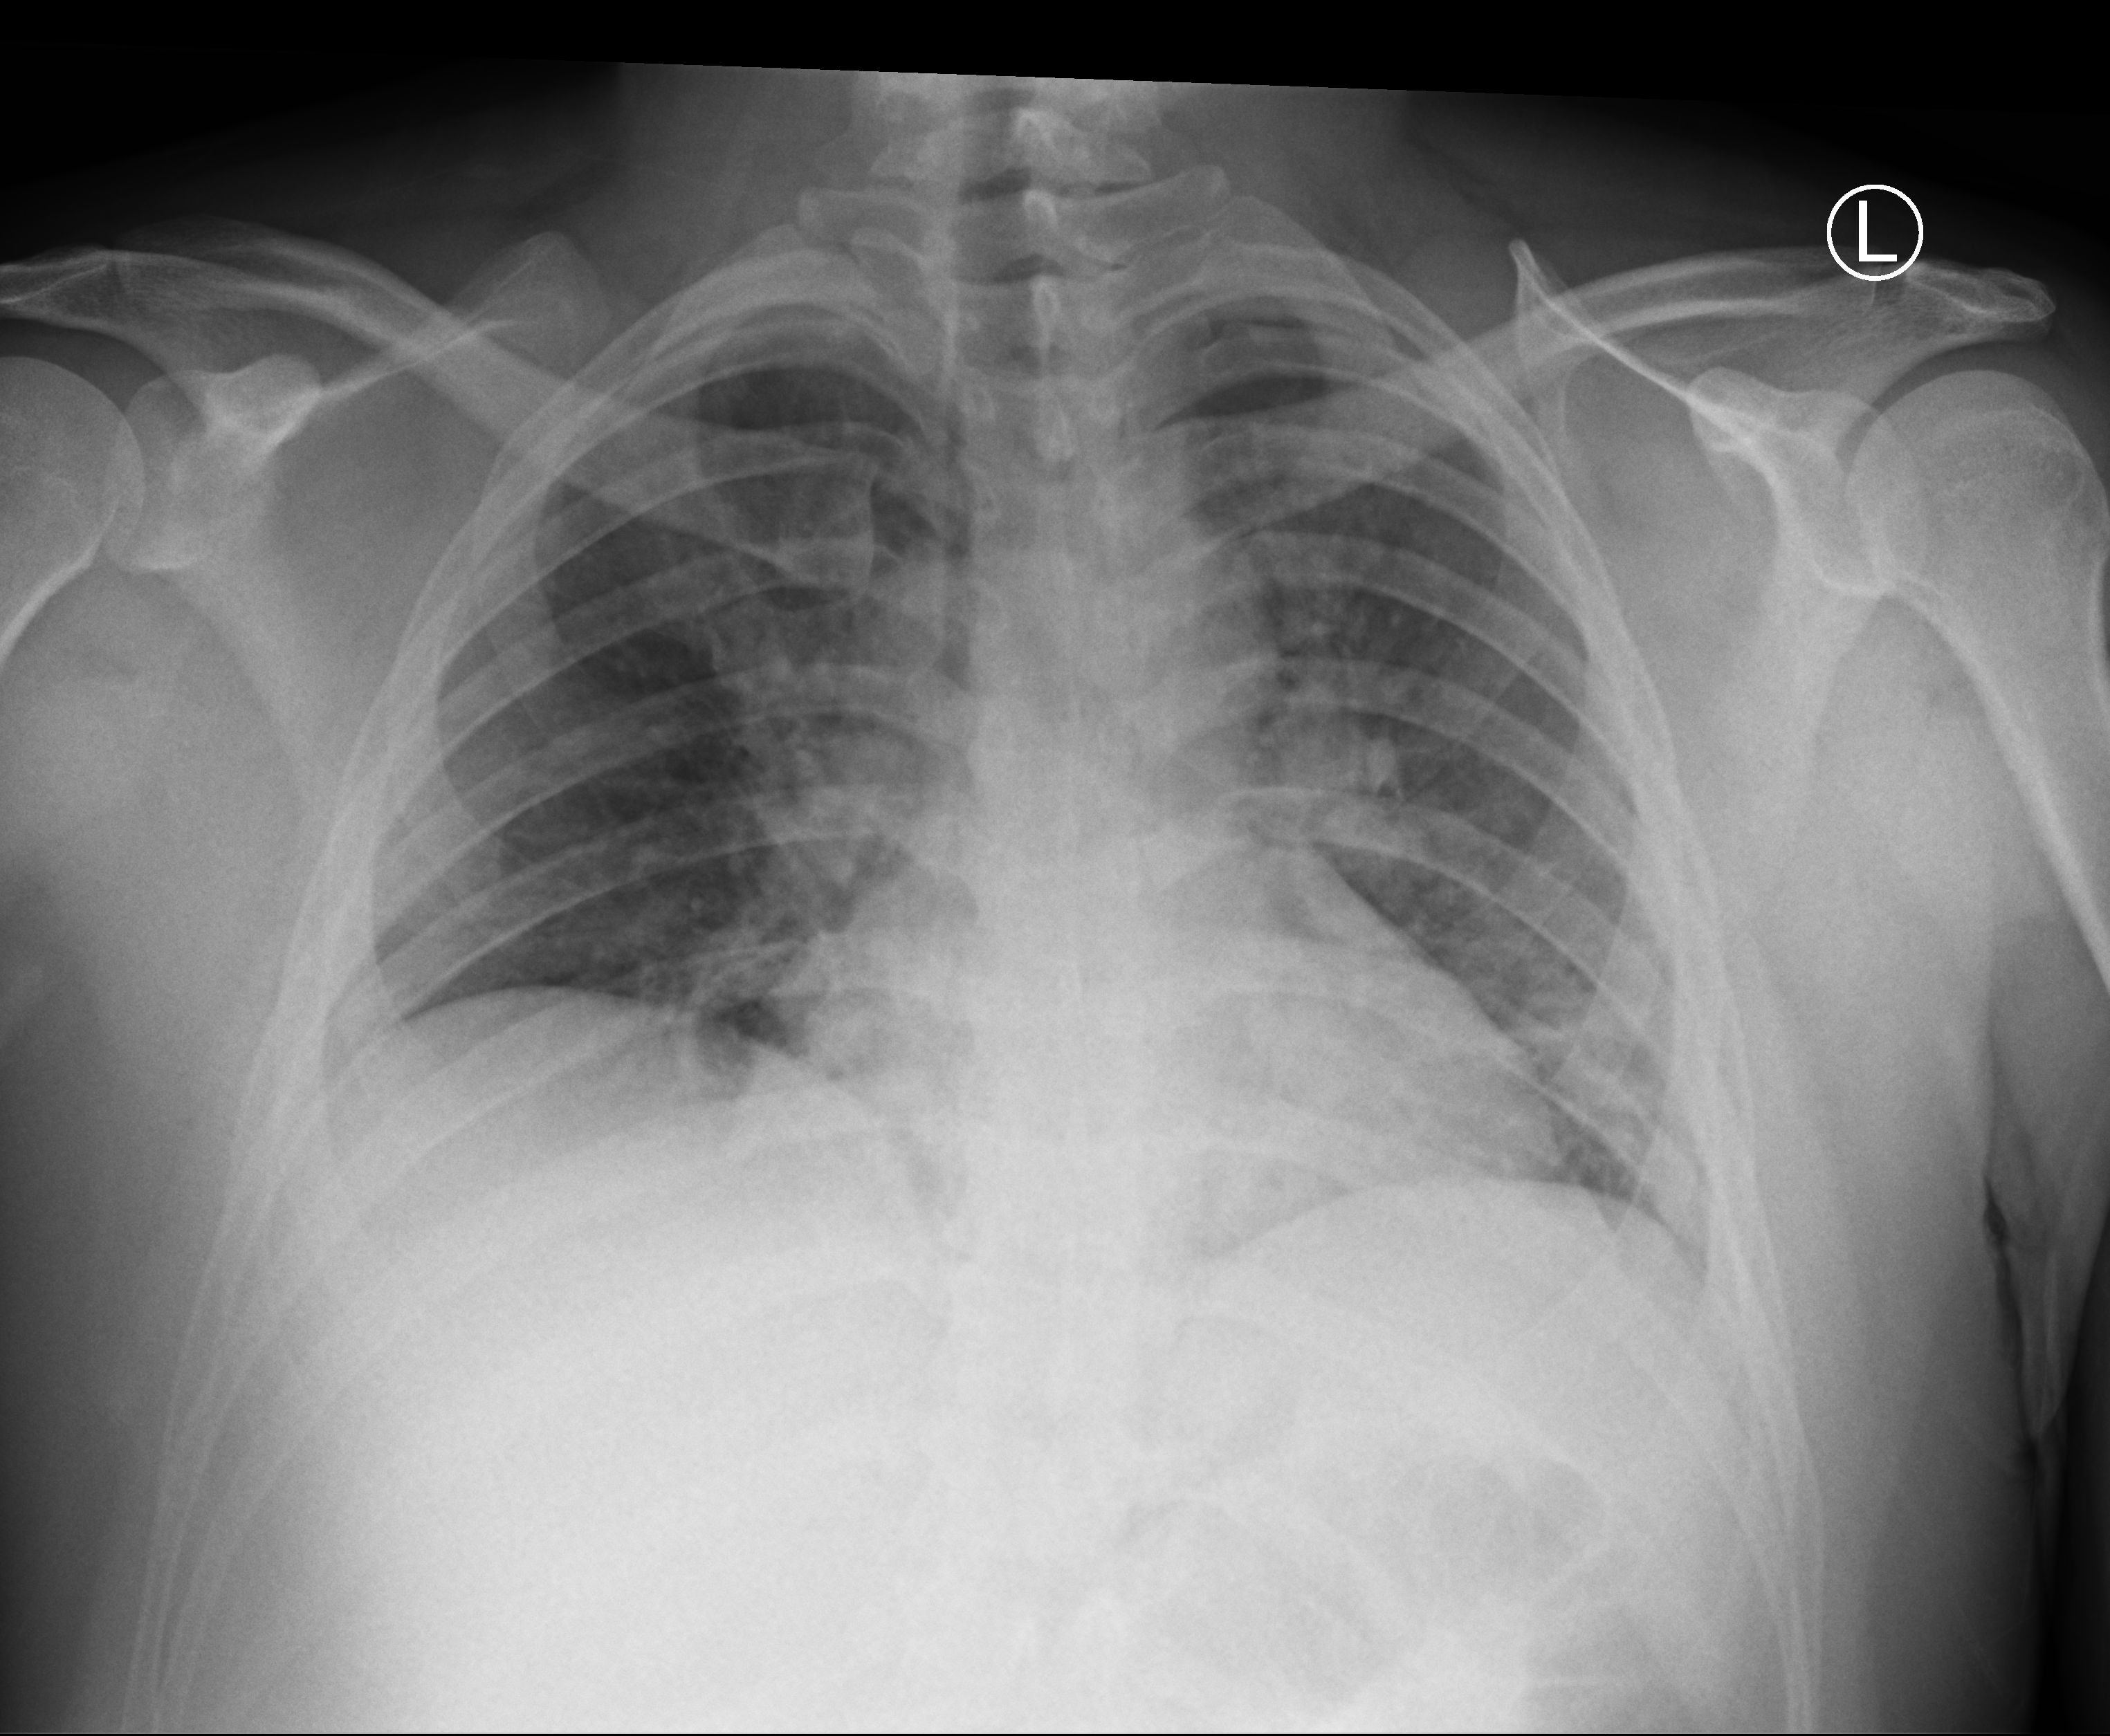
Bedside chest radiograph (computed radiography), anteroposterior (AP) projection. Patient hospitalised with COVID-19; male, aged 18–59 years.
Admission-level facts for this patient (not findings on this image; timing relative to this image not recorded): admitted to intensive care during this hospital stay: no; diabetes (admission record): no; mechanically ventilated during this hospital stay: no.